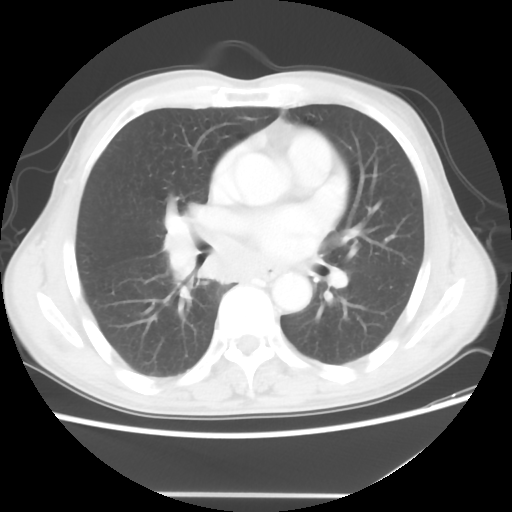
Chest CT, one axial slice. Reconstruction kernel STANDARD. Lung window (W 1500 / L -600 HU). 512 × 512 image matrix, field of view 344 × 344 mm. Male patient, age 65 years. From the clinical record (not read from this slice): clinical TNM (as recorded): T1c N3 M0; histopathological grade: G3.
Annotated regions visible in this slice (rectangle marked by the reading radiologist):
- lung tumour (recorded histology: small cell carcinoma): bounding box [x1, y1, x2, y2] px = [160, 211, 275, 286]